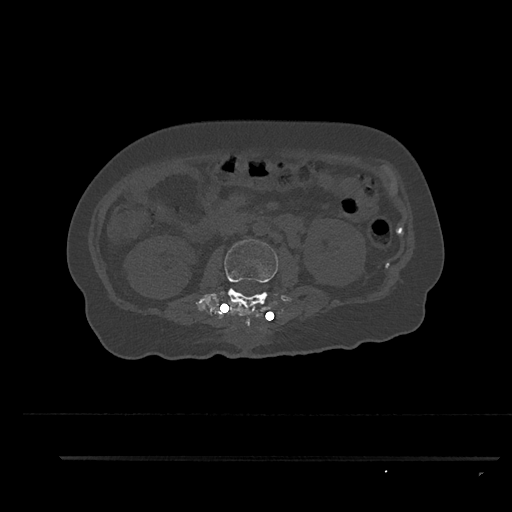
CT including the spine, one axial slice. Slice 147 of 797 in the series (ordered by position). 120 kVp. Bone window (W 1800 / L 400 HU). 512 × 512 image matrix, field of view 408 × 408 mm. Patient: female, 44 years. Case-level facts recorded for this patient, not image findings: primary cancer: renal; vertebrae with lytic lesions (as recorded): L1.
Structures marked on this image (semi-automatic segmentation, software-assisted and operator-edited):
- L2 vertebra: bounding box <195,239,278,326> (left, top, right, bottom; pixels)